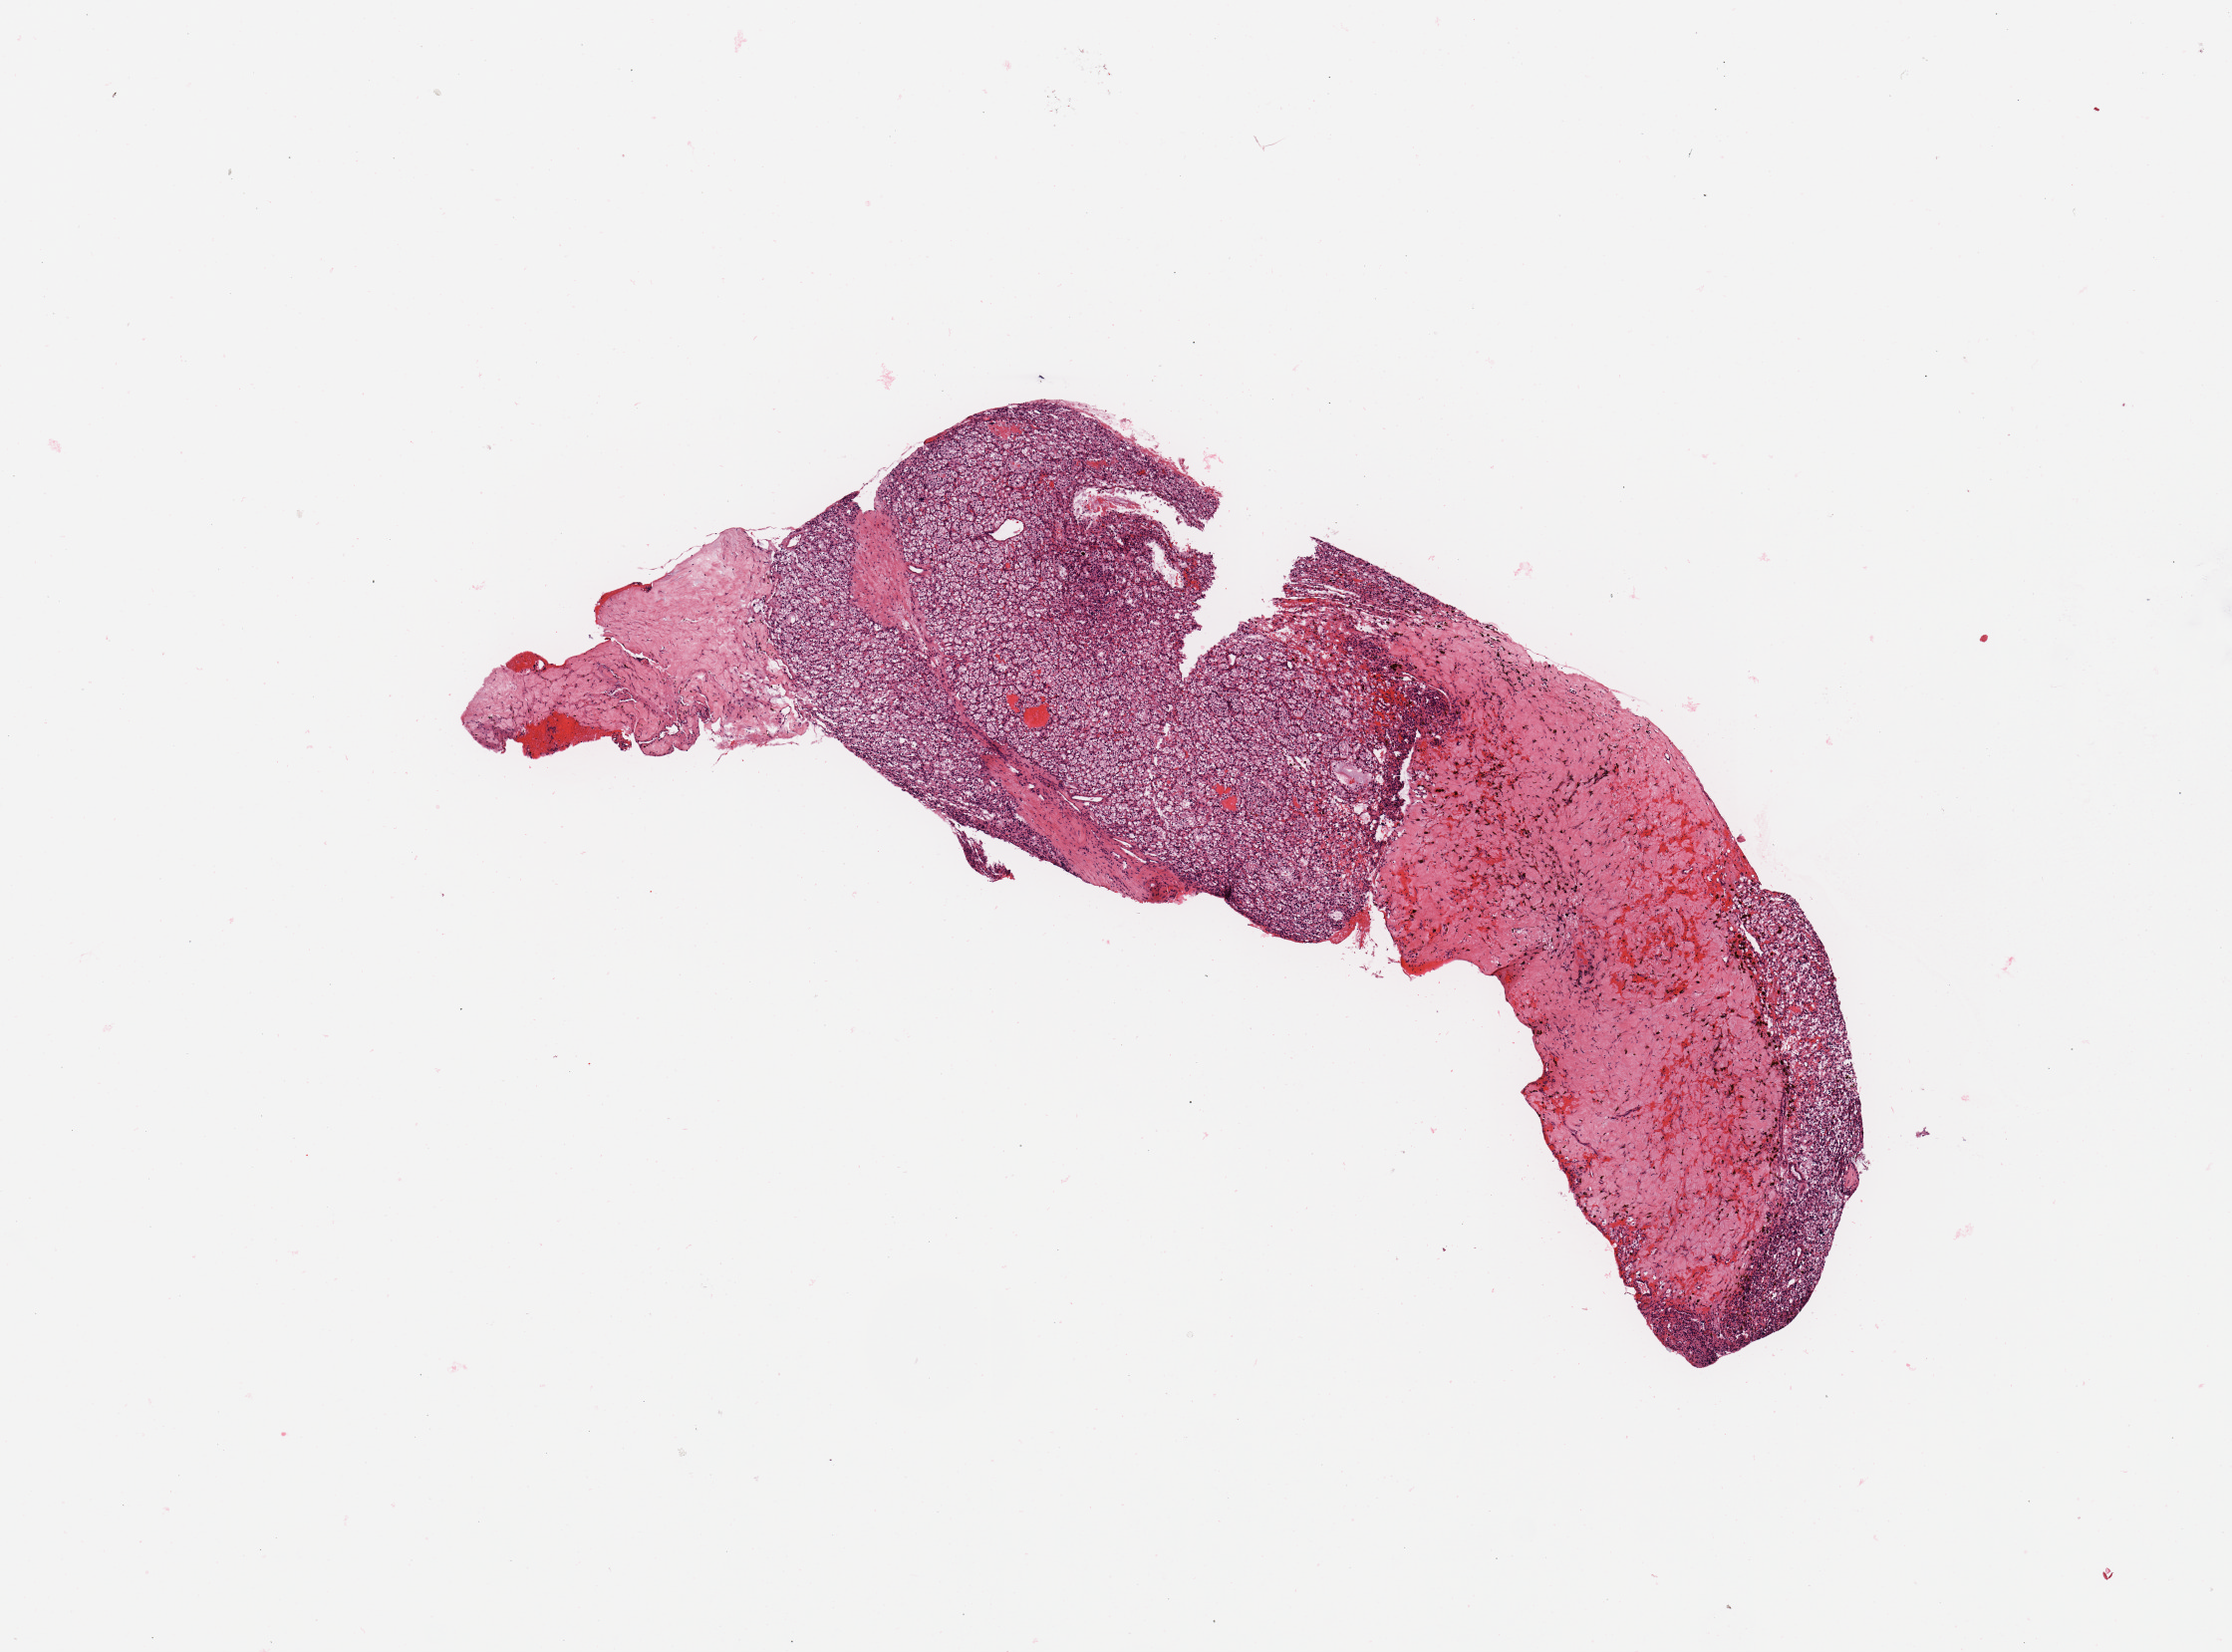
Hematoxylin and eosin (H&E) stained whole-slide image, low-resolution overview of the scanned area, about 8.9 x 6.6 mm (slide scanned at 20x). Tumour tissue sample, kidney. Patient: female, age 64 years. Histologic grade: G2 (moderately differentiated).
* AJCC pathologic stage: I
* diagnosis: Renal cell carcinoma, NOS
* primary tumour site (as recorded): lower pole